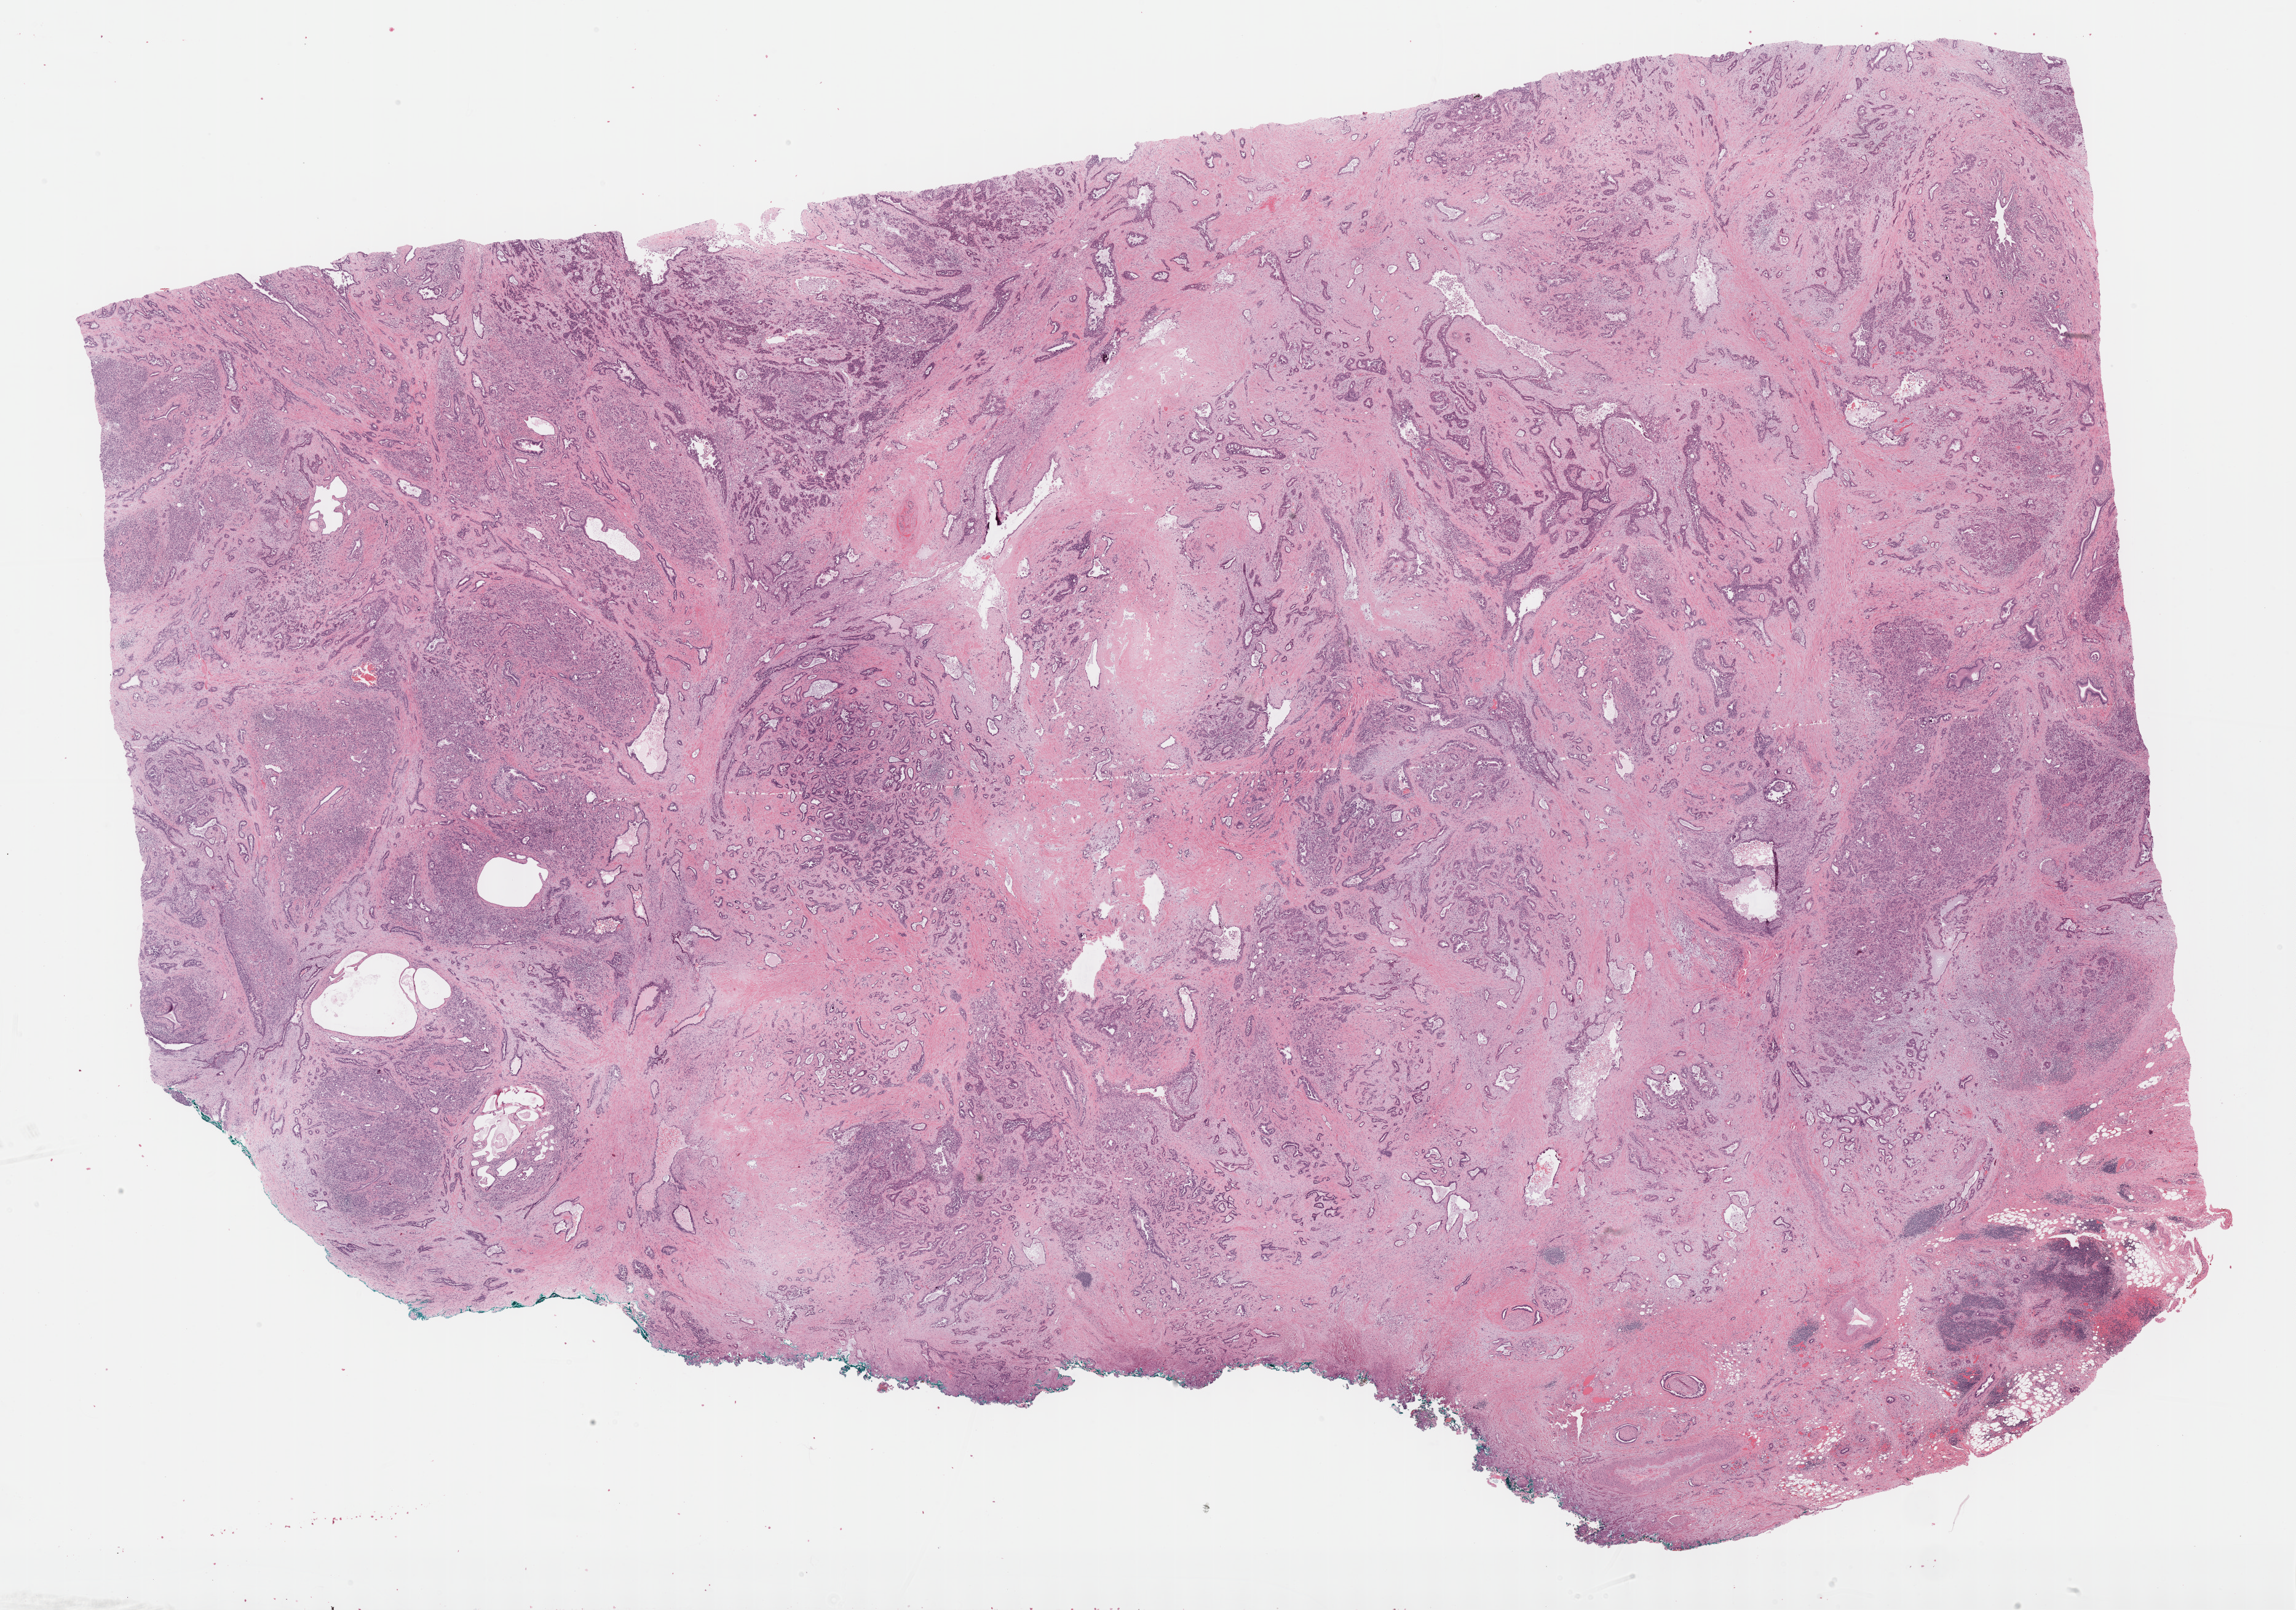
Digitized H&E tissue section (whole slide), whole scanned area (about 30.2 x 21.2 mm) shown as a low-resolution overview; formalin-fixed paraffin-embedded (FFPE) diagnostic section; sample: primary tumour, pancreas. Male, age 57 years at initial diagnosis.
Diagnosis: Infiltrating duct carcinoma, NOS (head of pancreas).